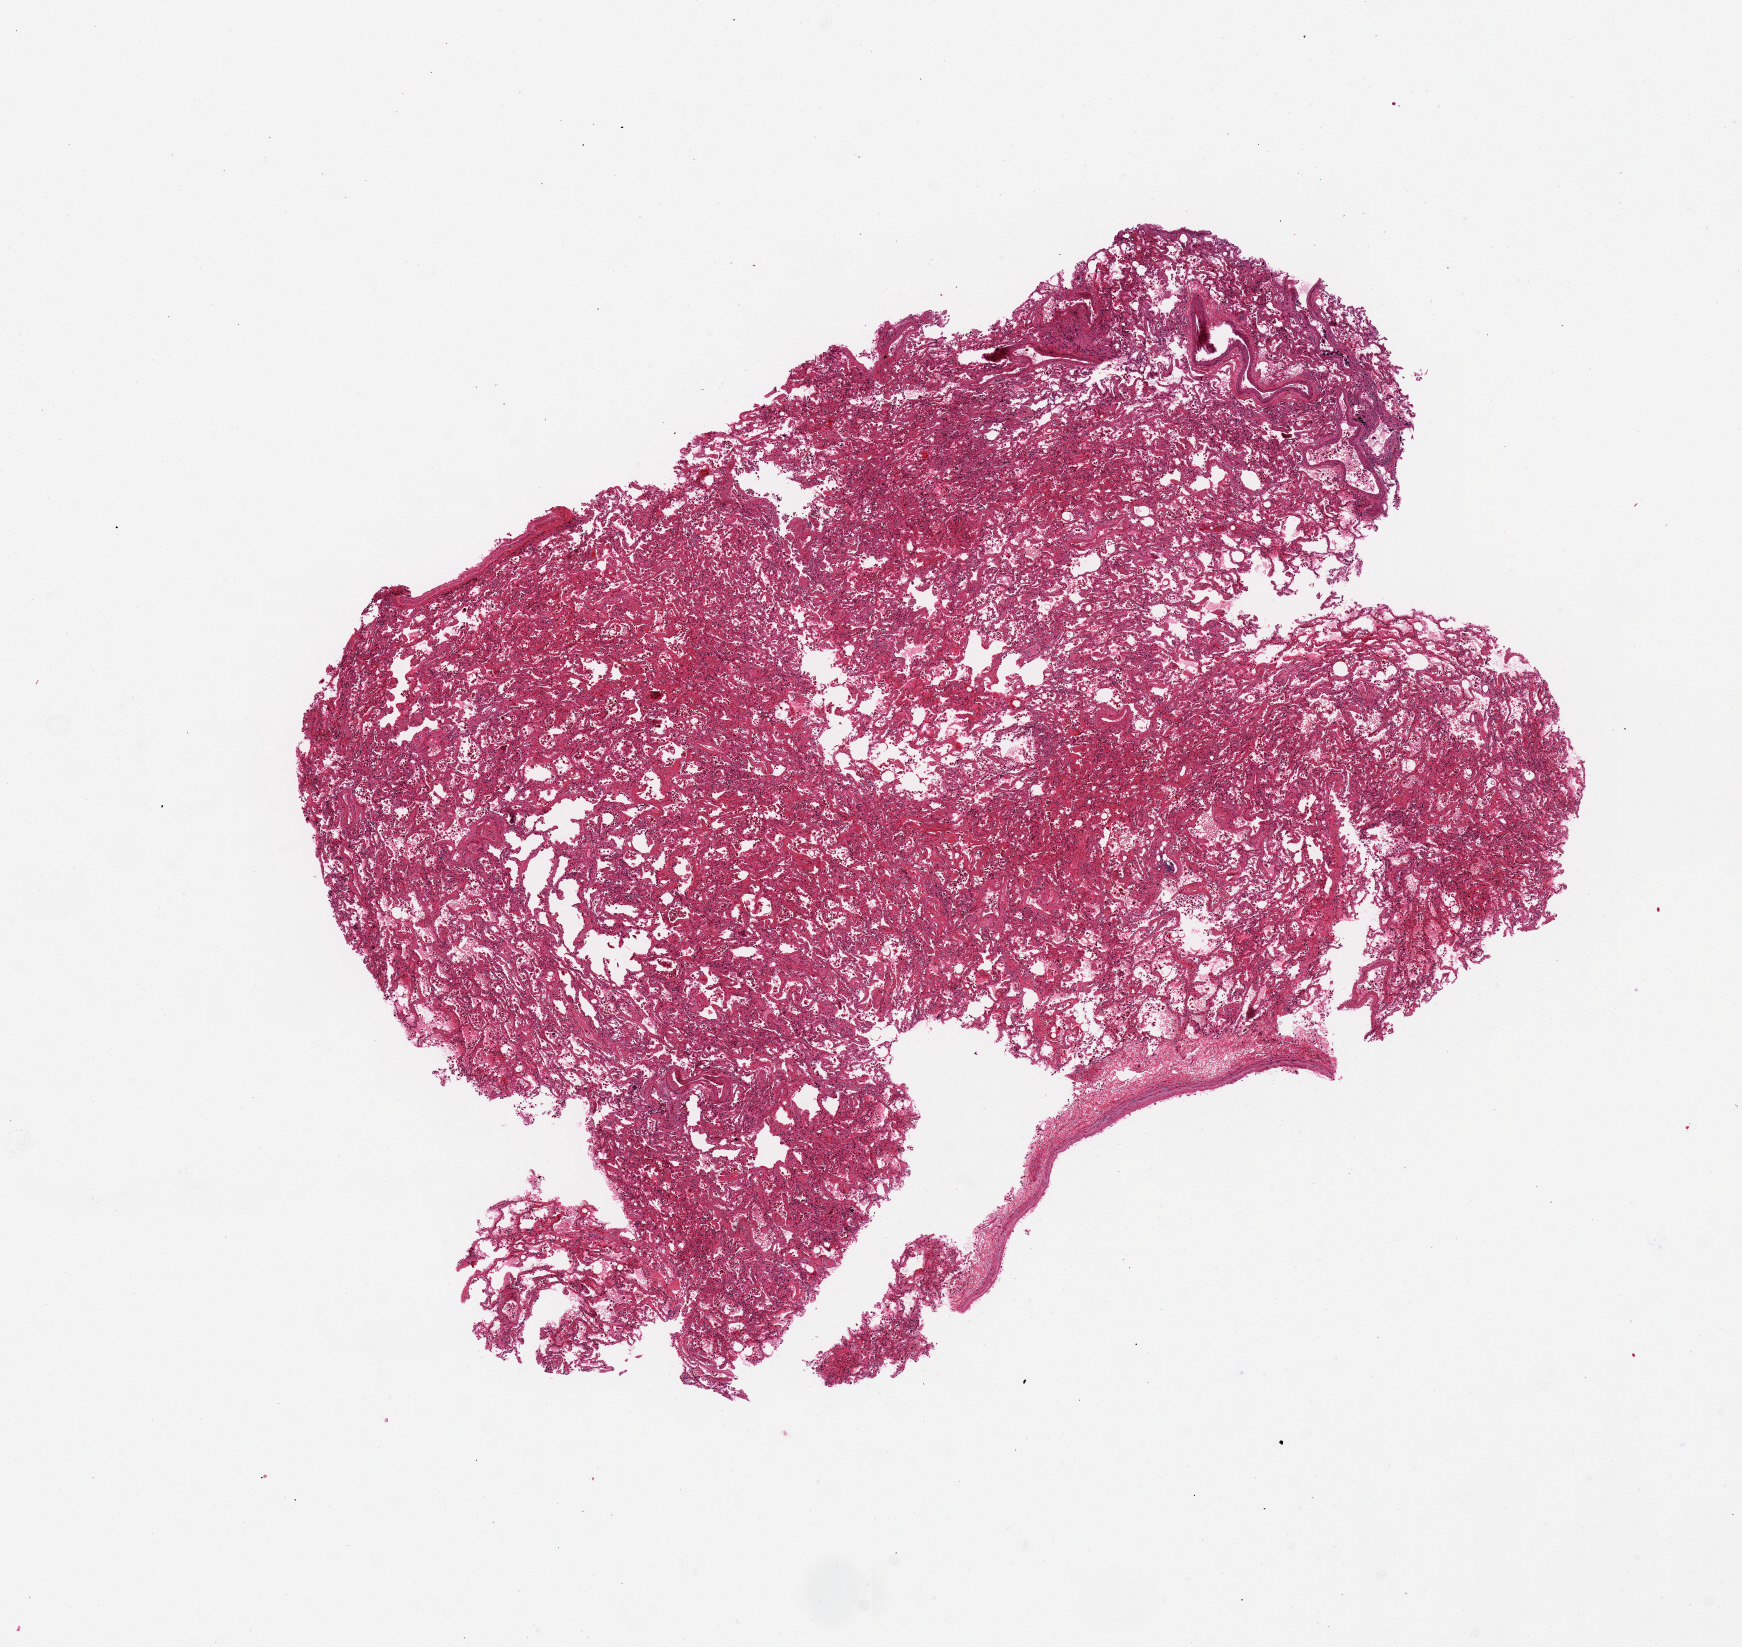
Hematoxylin and eosin (H&E) whole-slide image — a low-resolution overview of the entire scanned area, about 13.8 x 13.0 mm; PAXgene-fixed paraffin-embedded (PFPE) section; target tissue: lung; tissue donor sample. Donor: female.
Pathologist's review note for this sample: Mild-moderate congestion.